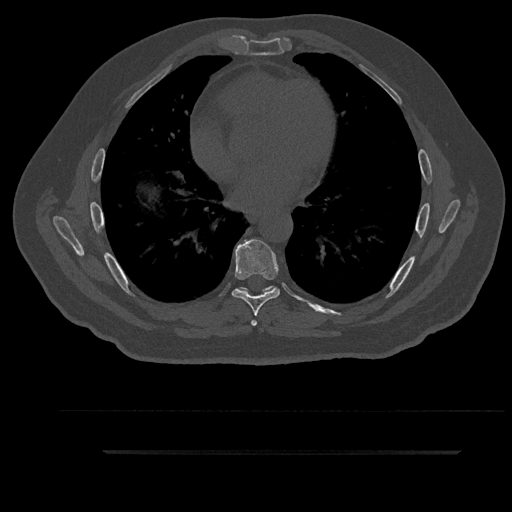
CT including the spine, one axial slice. Slice 519 of 797 in the series (ordered by position). Reconstruction kernel Br40s/3. 120 kVp. Bone window (W 1800 / L 400 HU). 0.5 mm slice thickness. 512 × 512 image matrix, field of view 432 × 432 mm. Patient: male, 63 years. From the clinical record (not read from this slice): primary cancer: renal; vertebrae with lytic lesions (as recorded): T8.
Outlined on this slice (semi-automatically segmented with operator editing):
- T6 vertebra: bounding box [x1, y1, x2, y2] px = [237, 286, 275, 326]
- T7 vertebra: [232, 239, 280, 316]
- T8 vertebra: [241, 285, 273, 291]